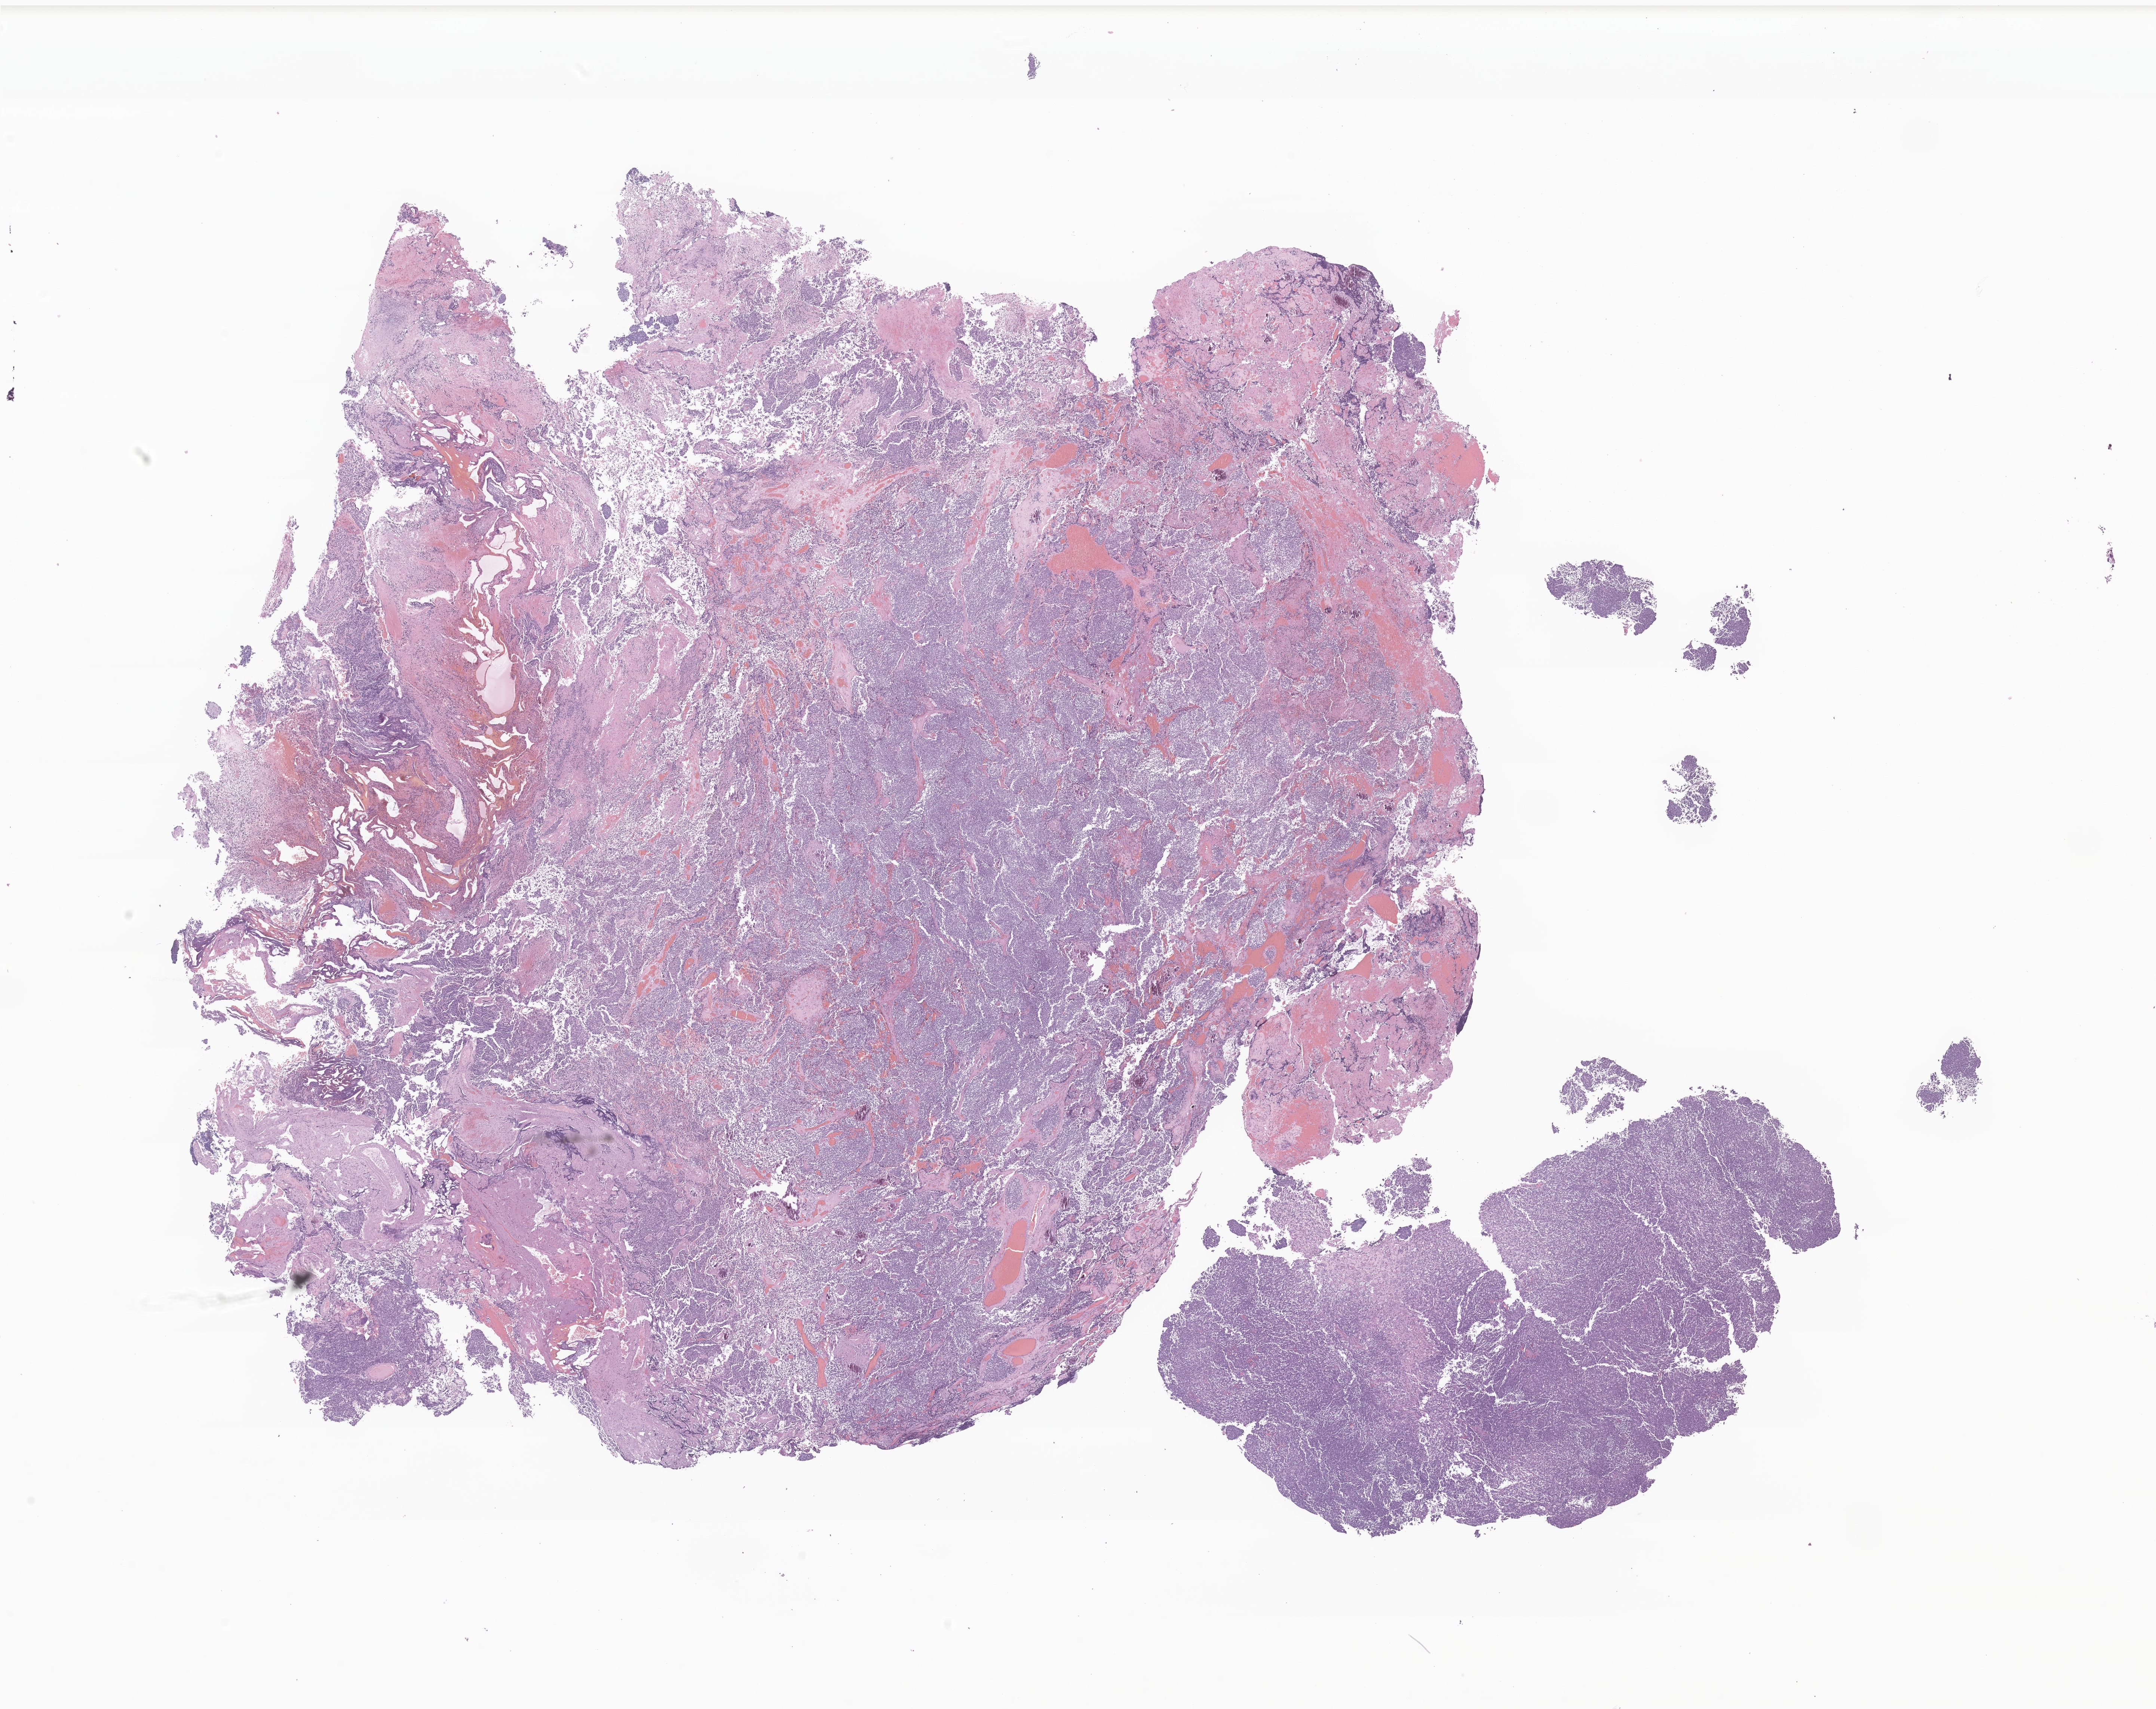
Haematoxylin and eosin whole-slide image of tumor tissue from the choroid of eye, shown as a low-resolution overview of the whole scanned area (about 24.3 x 19.3 mm). Formalin-fixed, paraffin-embedded (FFPE) tissue. Female patient, age 46 months (3 years 10 months).
Diagnosis (ICD-O-3 morphology term): Choroid plexus papilloma, NOS.